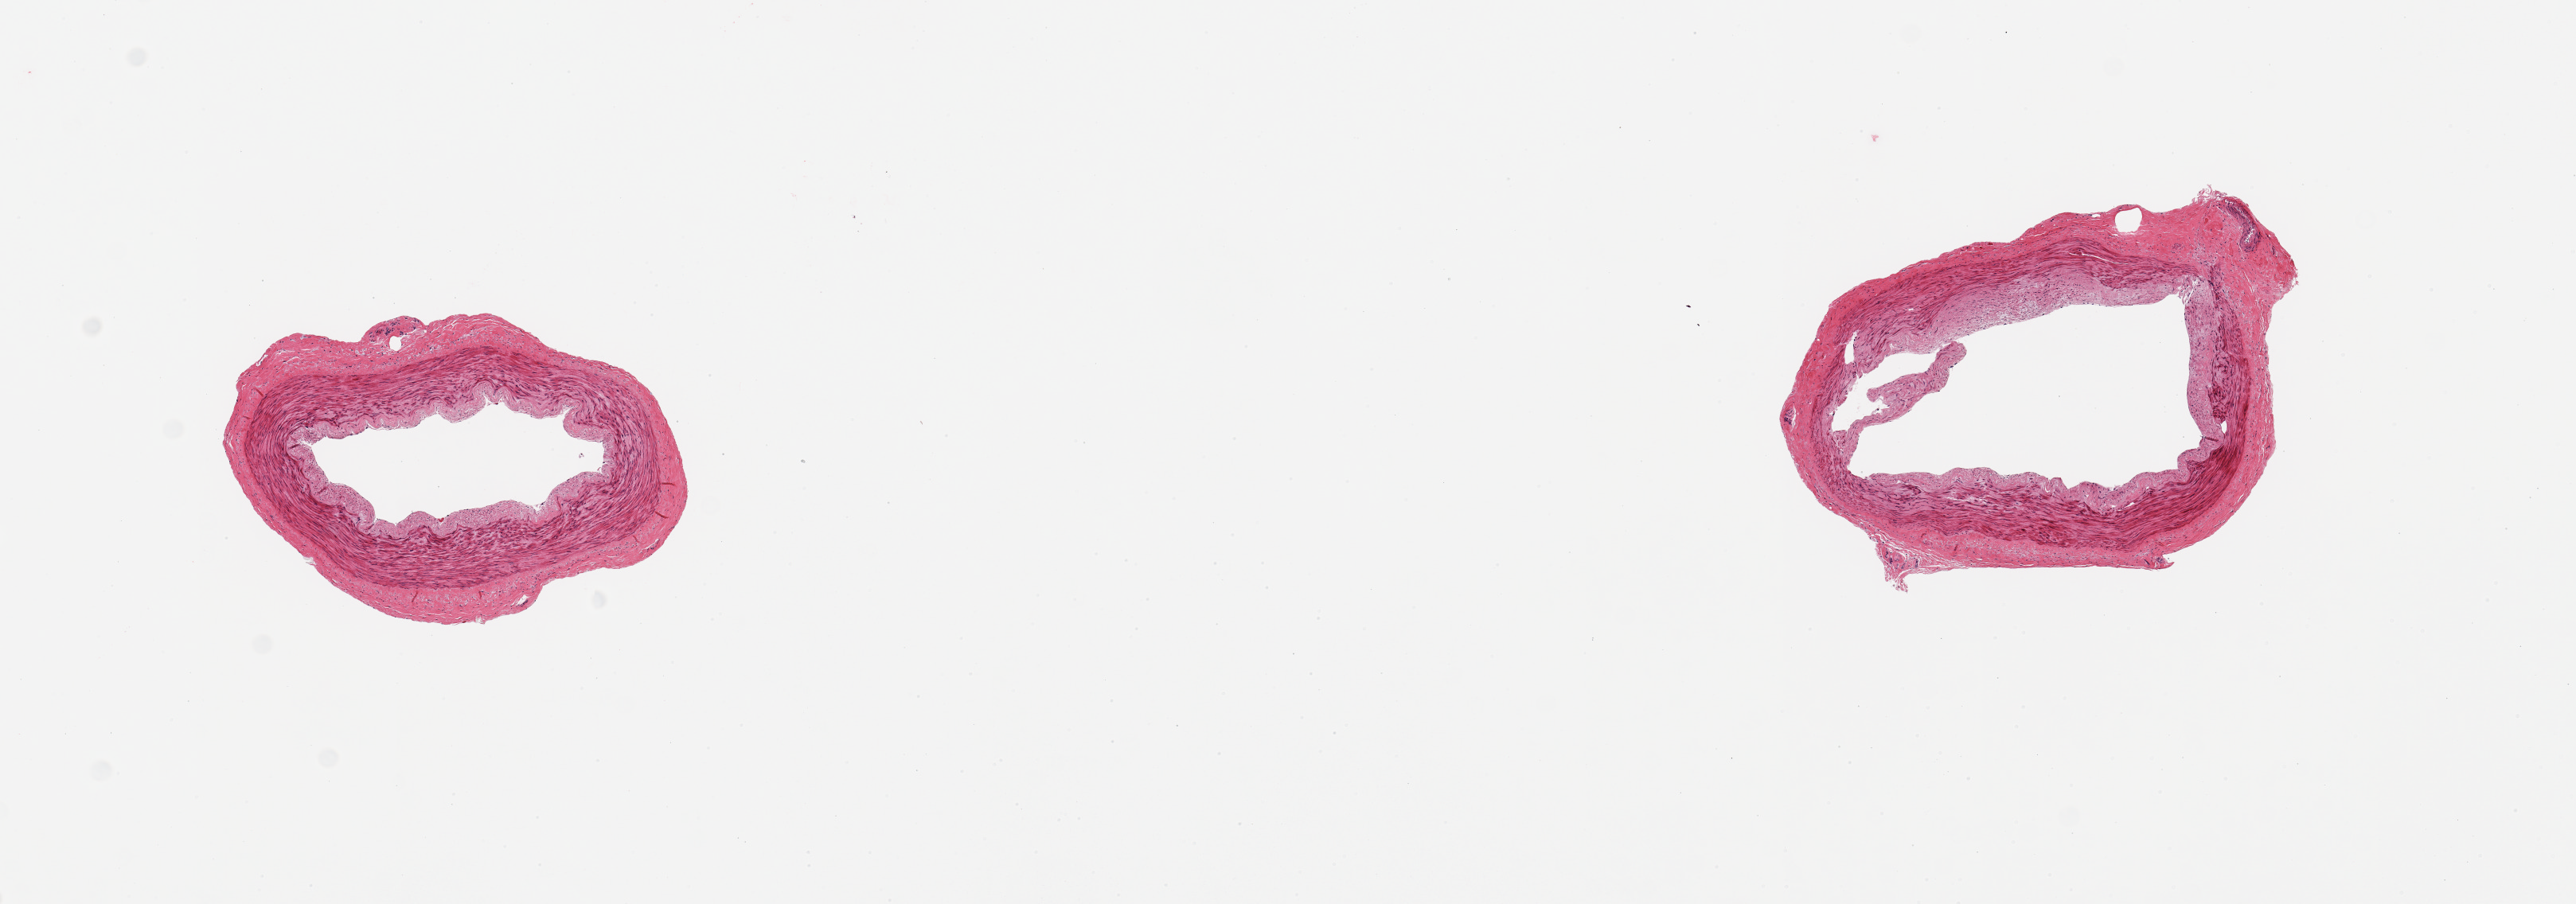
Digitized haematoxylin and eosin-stained section, shown as a low-resolution overview of the whole scanned area (about 12.8 x 4.5 mm, from a 20x scan). PAXgene-fixed paraffin-embedded (PFPE) section. Sampled site (target tissue): tibial artery. Donor tissue sample. Donor: male.
Review note (as recorded): 2 pieces; early atheromatous change, well trimmed.